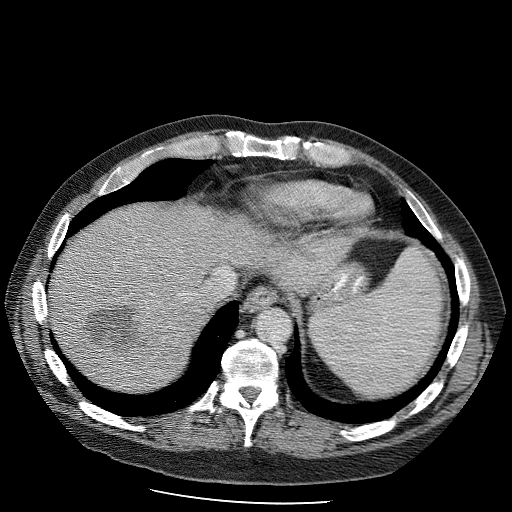
Contrast-enhanced abdominal CT (liver protocol), one axial slice. Position 87 of 98 along the scan axis. 120 kVp. Soft-tissue window (W 400 / L 40 HU). 2.5 mm slice thickness. 512 × 512 image matrix, field of view 400 × 400 mm. From the clinical record (not read from this slice): diagnosis: hepatocellular carcinoma (patient treated with transarterial chemoembolisation; whether this scan precedes or follows treatment is not stated here); TNM stage (as recorded): Stage-II; Child-Pugh class: B; tumour differentiation: moderately differentiated; tumour nodularity: uninodular.
Outlined on this slice (semi-automatic segmentation, software-assisted and operator-edited):
- liver parenchyma outside the tumour (the mass and vessels are separate outlines, so this box may not span the whole liver): bounding box (x1, y1, x2, y2) in pixels: (50, 208, 252, 384)
- mass: (81, 302, 142, 349)